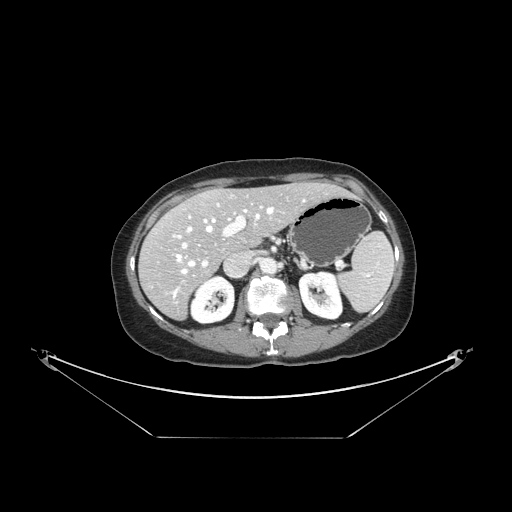
Contrast-enhanced abdominal CT, one axial slice; slice 89 of 148 in the series (ordered by position); reconstruction kernel STANDARD; 120 kVp; intravenous contrast given; soft-tissue window (W 400 / L 40 HU); 2.5 mm slice thickness; 512 × 512 image matrix. Female patient, age 73 years. From the clinical record (not read from this slice): diagnosis: colorectal cancer liver metastases, imaged before liver resection; multiple liver metastases: no; largest metastasis: 1 cm; chemotherapy before resection: yes.
Outlined on this slice (expert manual segmentation):
- hepatic veins: bounding box [x1, y1, x2, y2] px = [173, 206, 274, 297]
- liver: [140, 184, 345, 318]
- planned liver remnant (the part of the liver to remain after resection): [168, 184, 343, 254]
- portal vein (with intrahepatic branches): [173, 204, 262, 267]